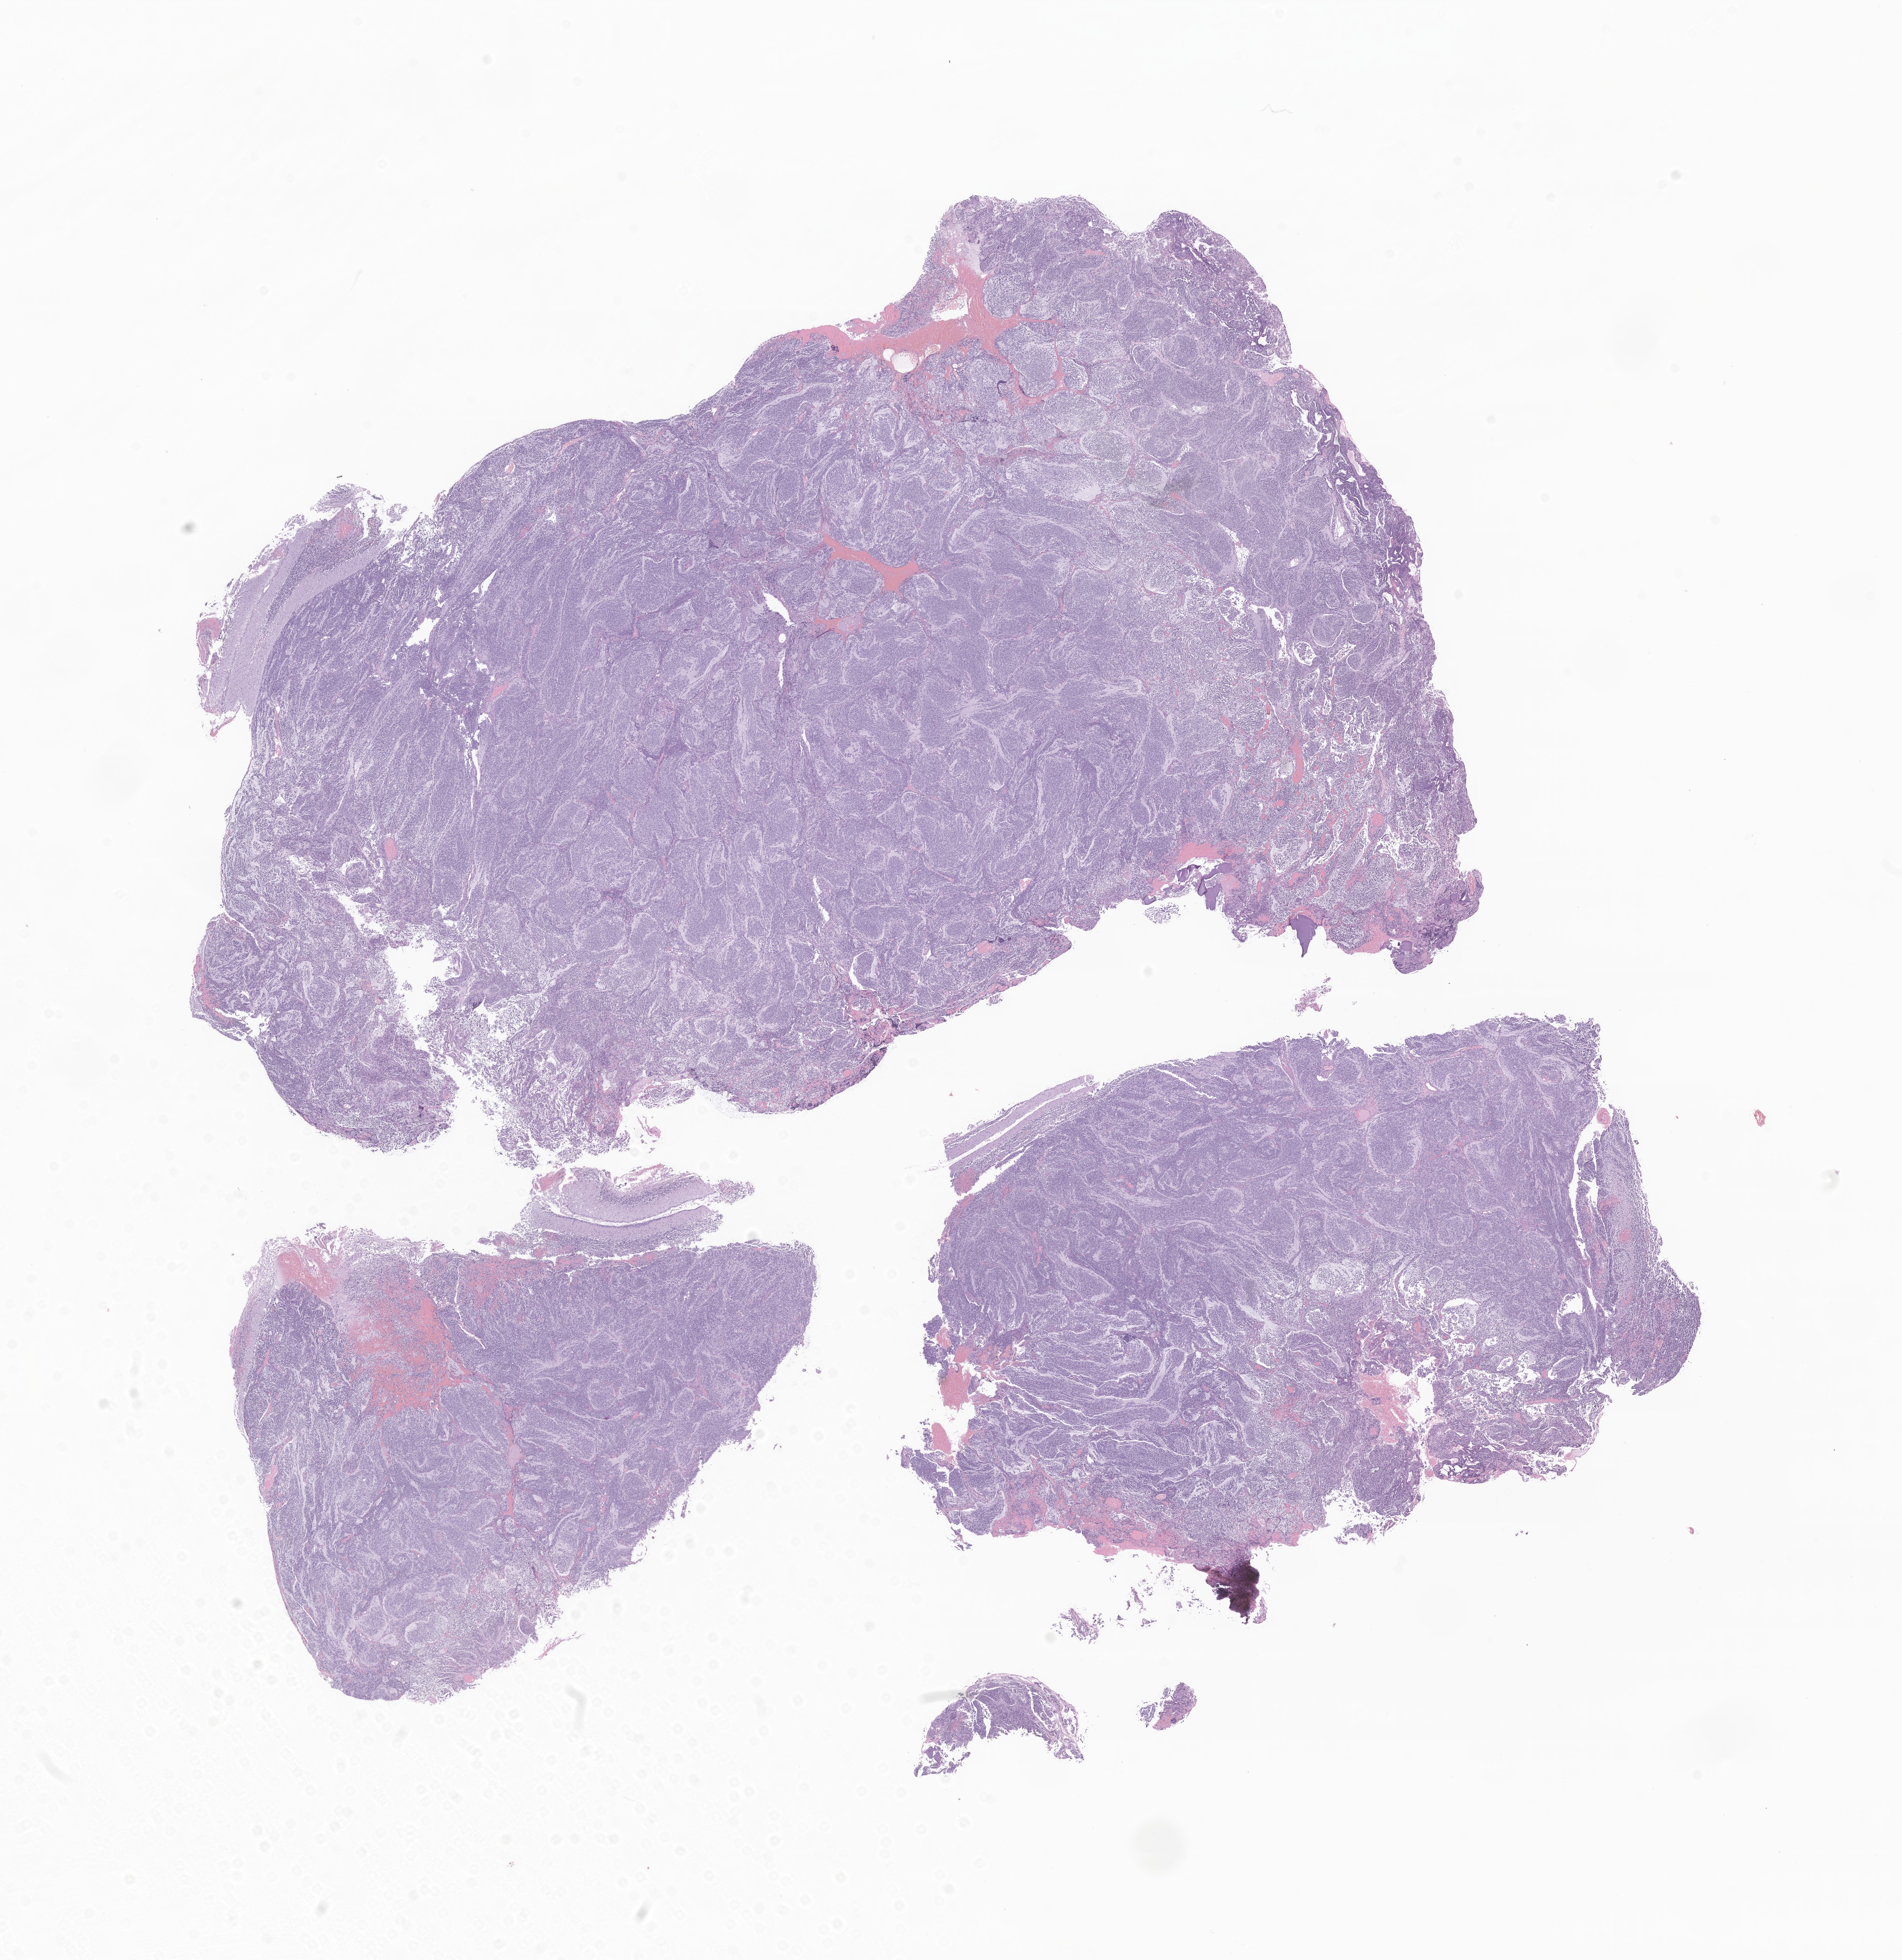
Digitized H&E-stained section of tumor tissue from the cerebellum, shown as a low-resolution overview of the whole scanned area (about 18.4 x 19.0 mm), FFPE section. Male patient, age 348 days.
Recorded diagnosis: Desmoplastic nodular medulloblastoma.